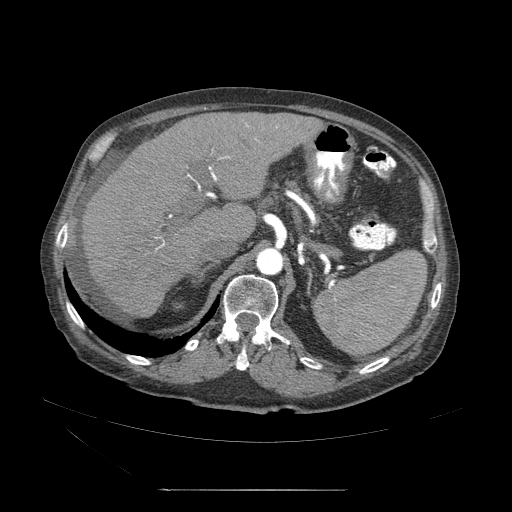
Contrast-enhanced abdominal CT (liver protocol), one axial slice. Slice 30 of 71 in the series (ordered by position). Reconstruction kernel STANDARD. Soft-tissue window (W 400 / L 40 HU). 2.5 mm slice thickness. 512 × 512 image matrix, field of view 440 × 440 mm. From the clinical record (not read from this slice): diagnosis: hepatocellular carcinoma (patient treated with transarterial chemoembolisation; whether this scan precedes or follows treatment is not stated here); TNM stage (as recorded): Stage-II; Child-Pugh class: A.
Annotated regions visible in this slice (semi-automatic segmentation, software-assisted and operator-edited):
- abdominal aorta: box from (x=257, y=246) to (x=284, y=276) px
- liver parenchyma outside the tumour (the mass and vessels are separate outlines, so this box may not span the whole liver): (x=82, y=113)–(x=321, y=321)
- liver vessels: (x=130, y=159)–(x=238, y=271)